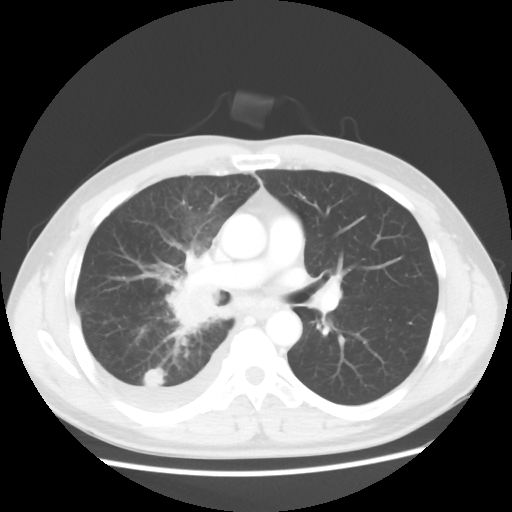
Chest CT, one axial slice. Slice 31 of 56 in the series (ordered by position). Reconstruction kernel STANDARD. Lung window (W 1500 / L -600 HU). 512 × 512 image matrix, field of view 360 × 360 mm. Patient: male, 46 years. From the clinical record (not read from this slice): clinical TNM (as recorded): T2 N3 M1.
Structures marked on this image (bounding box drawn by a radiologist):
- lung tumour (recorded histology: adenocarcinoma): bounding box <159,275,226,336> (left, top, right, bottom; pixels)